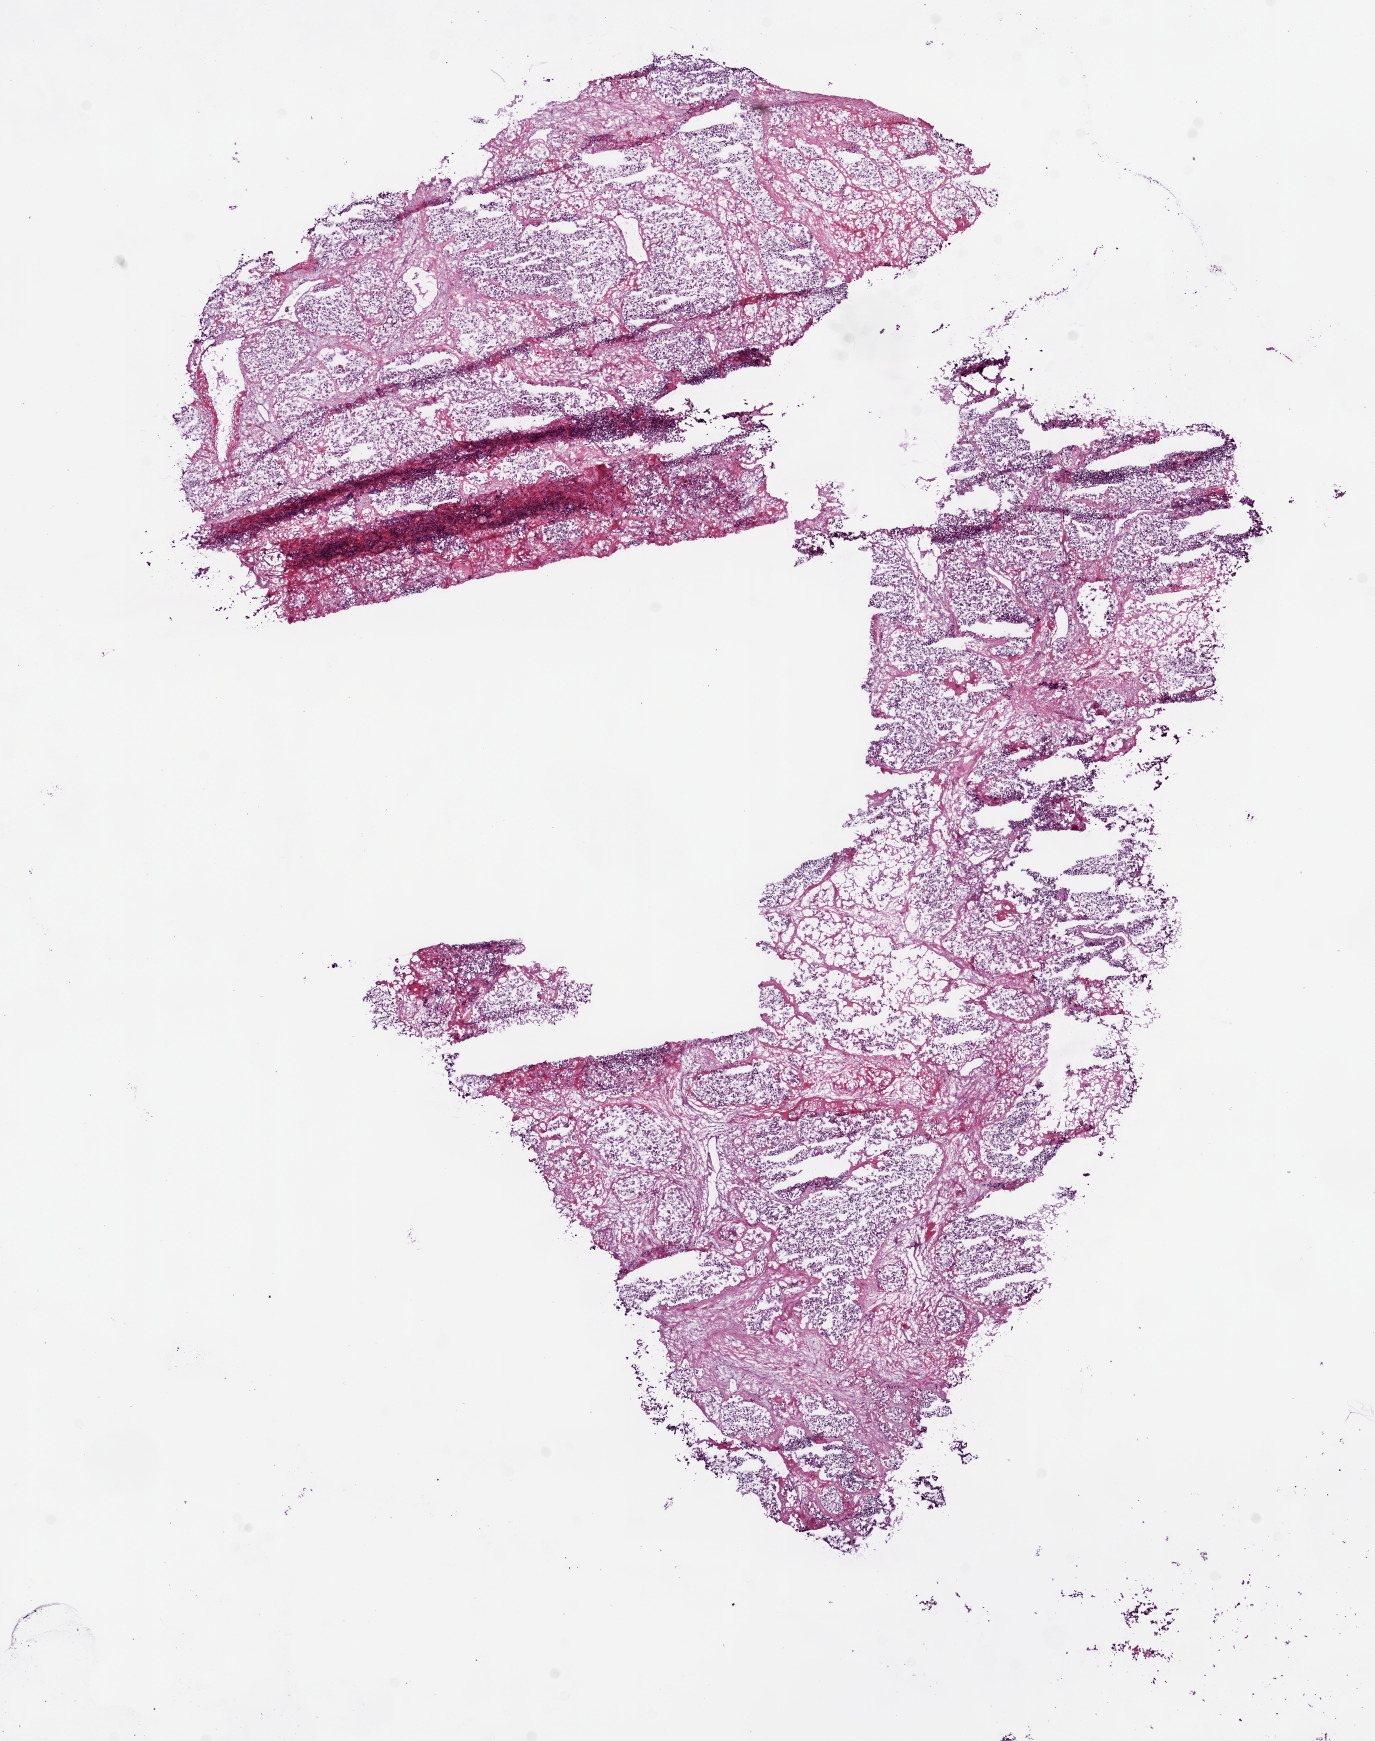
H&E whole-slide image — a low-resolution overview of the entire scanned area, about 11.0 x 14.0 mm (acquisition: 20x scan), frozen section from the bottom of the tissue portion, sample: primary tumour, kidney. Patient: male, age at initial diagnosis 60 years. Histologic grade: G4 (undifferentiated). Composition of this section per pathologist review: tumour cells 85%, tumour nuclei 85%, normal cells 0%, stromal cells 15%, necrosis 0%.
• diagnosis: Clear cell adenocarcinoma, NOS
• AJCC pathologic stage: IV